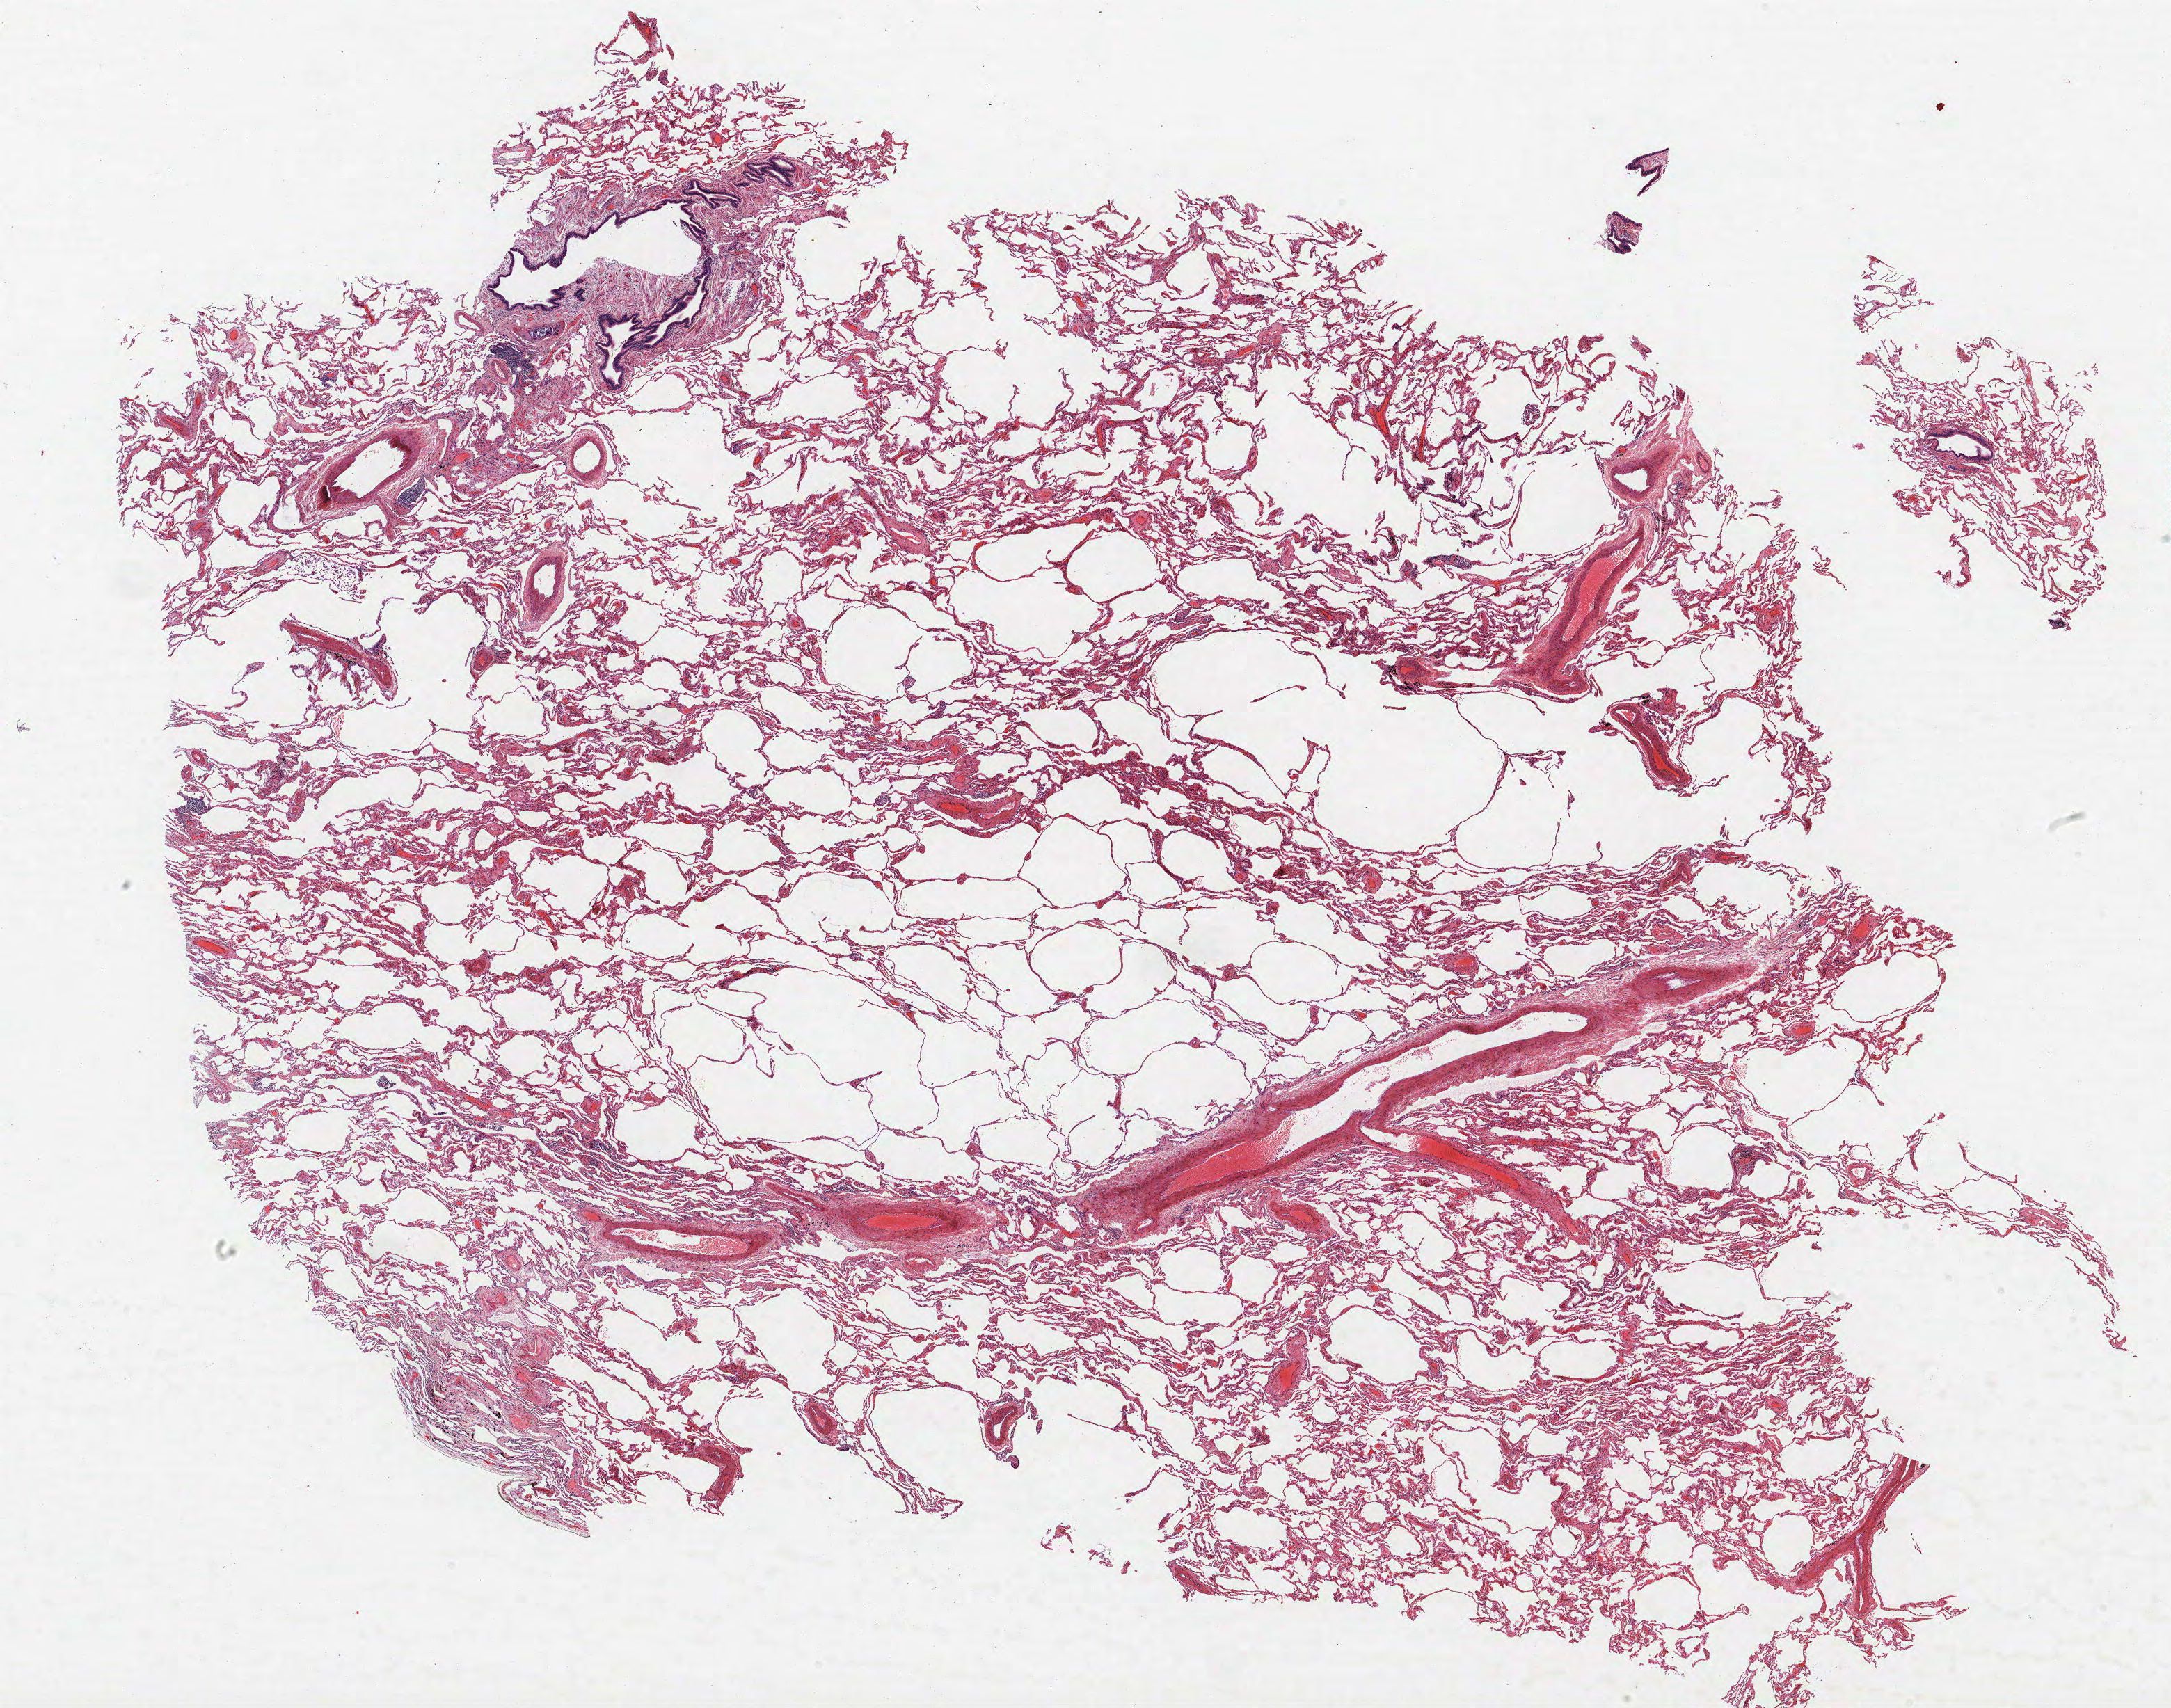
H&E whole-slide image, low-resolution overview of the scanned area, about 25.0 x 19.6 mm (slide scanned at 40x), formalin-fixed paraffin-embedded (FFPE) section, lung. Female, age 66 at enrolment. Former smoker at enrolment. Grade: moderately differentiated (G2).
Tumour size (pathology): 60 mm. Participant's lung-cancer diagnosis: Adenocarcinoma, NOS (ICD-O-3 8140/3). ICD-O-3 topography: lower lobe of lung (C34.3). Primary tumour location (clinical record): right lower lobe. Stage (AJCC 6th edition): IV.